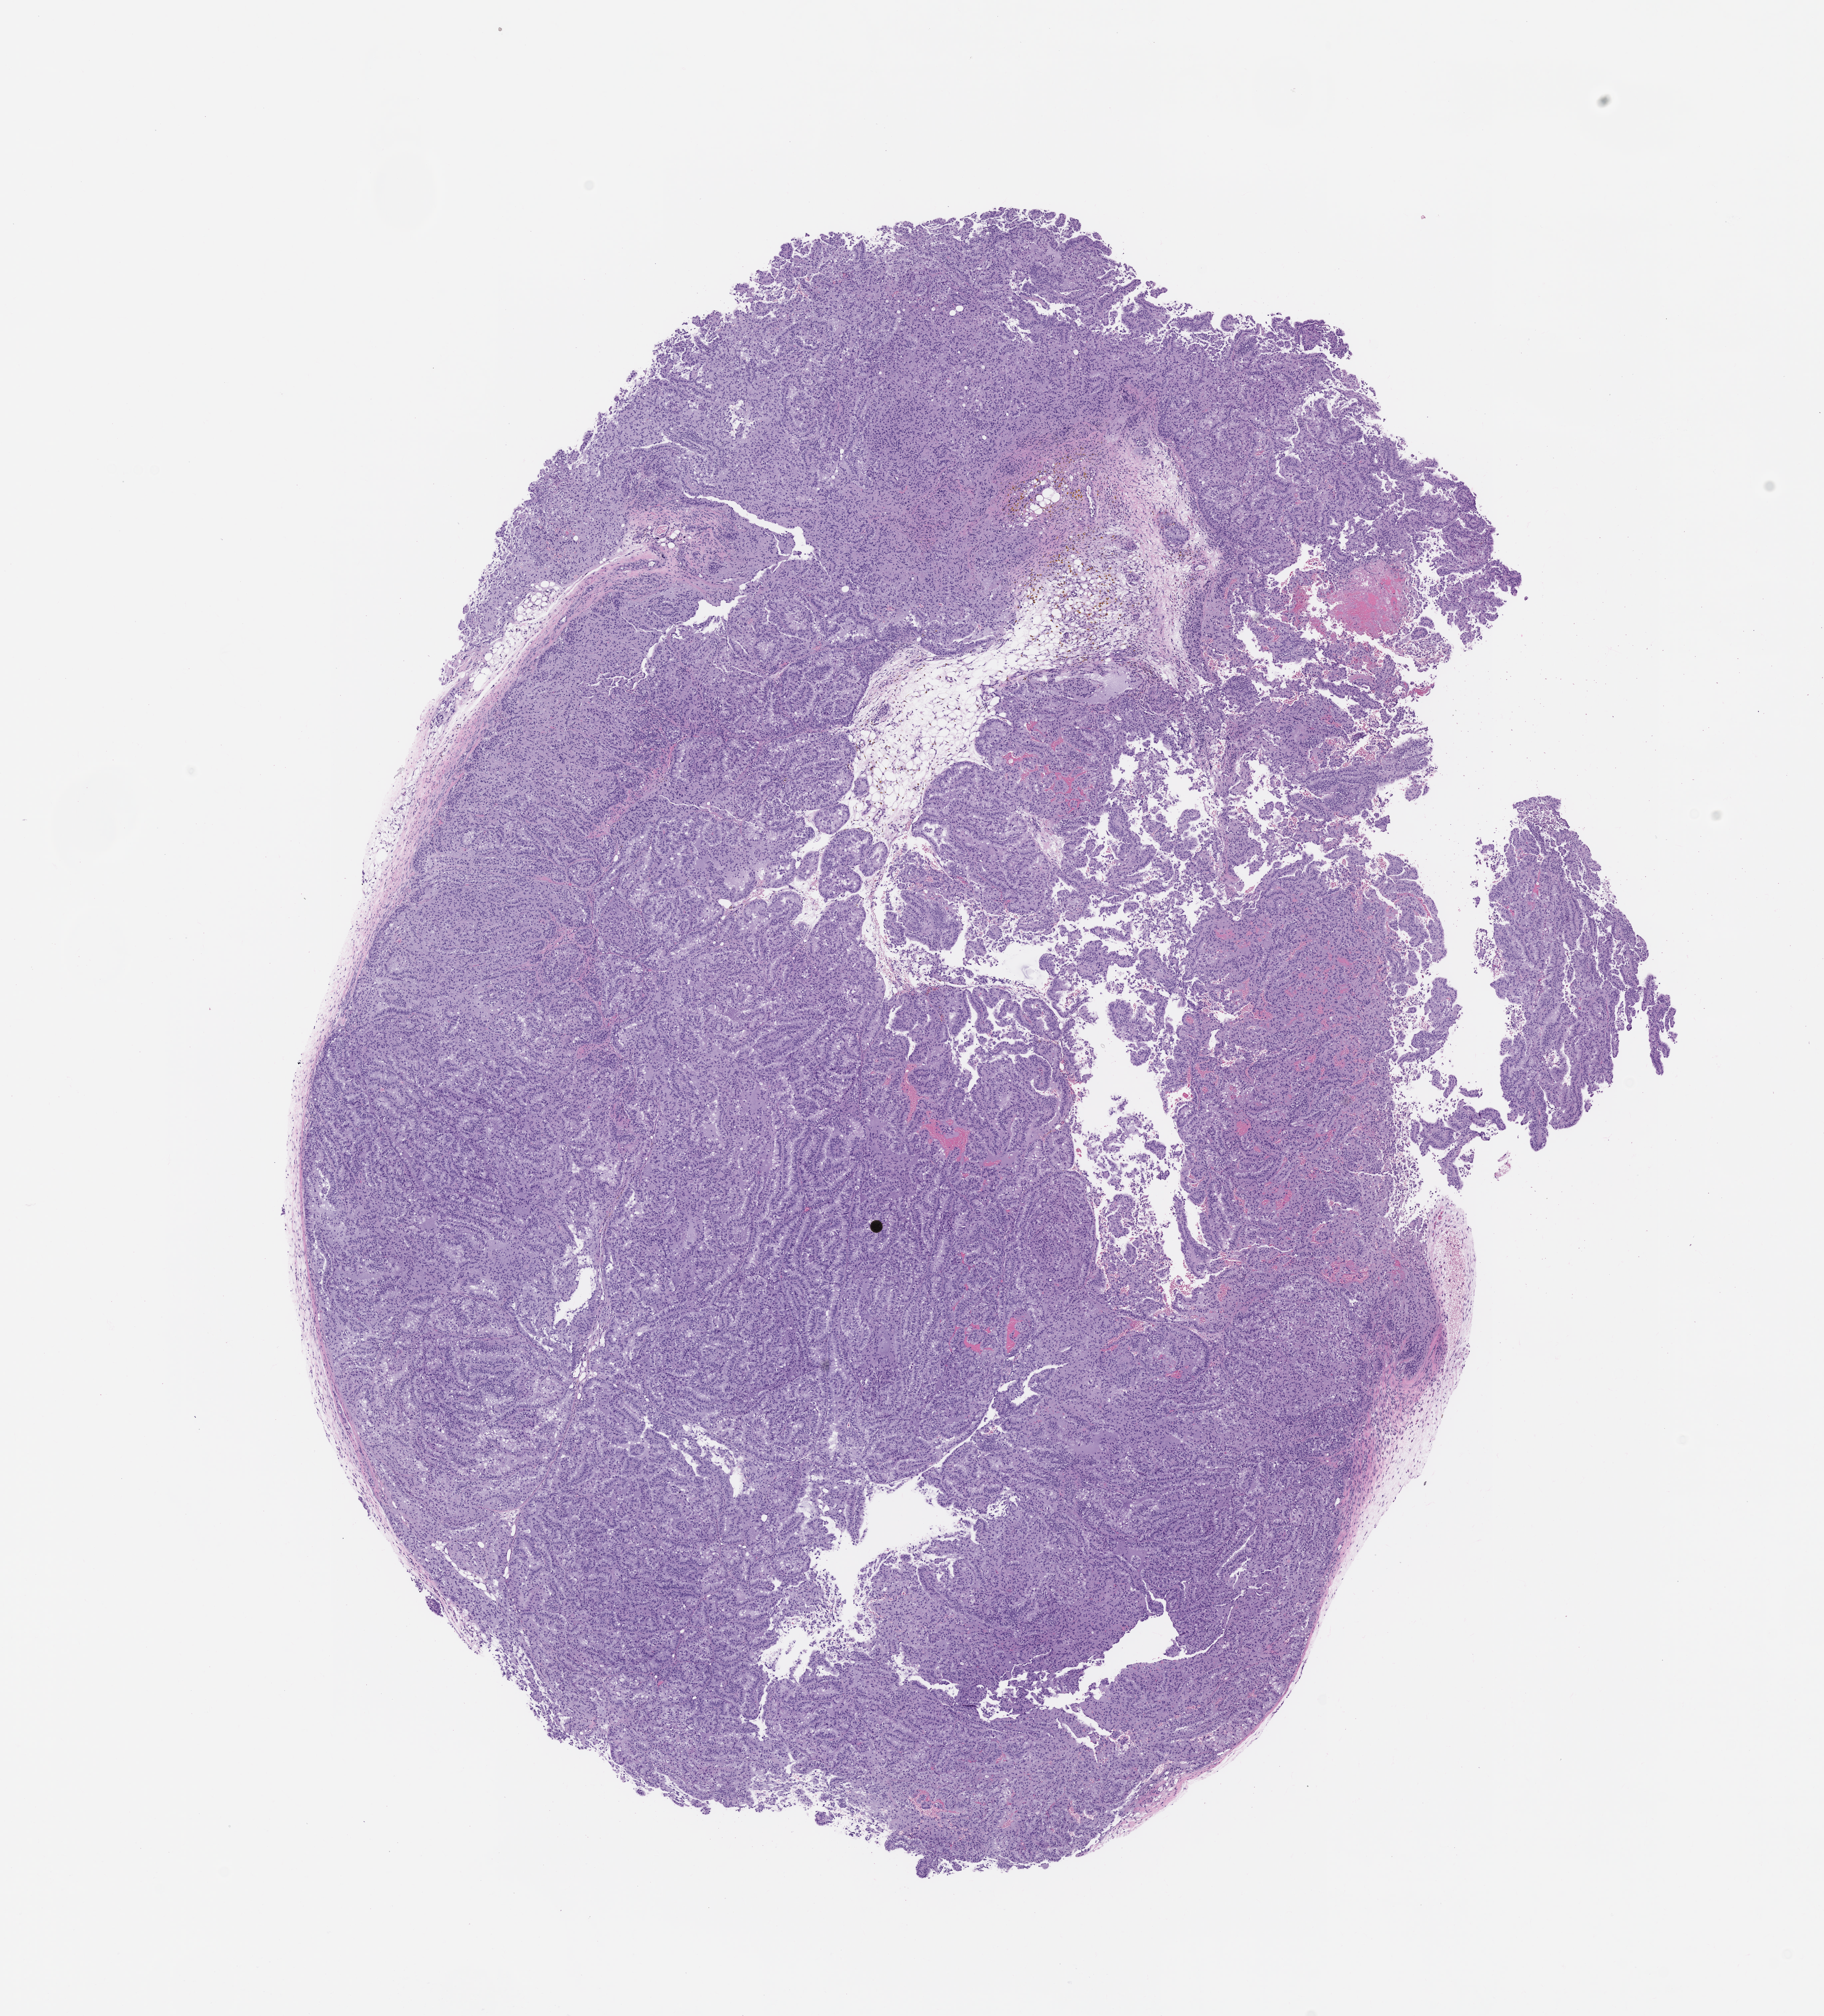
Haematoxylin and eosin whole-slide image of a patient-derived xenograft (PDX) tumor grown in a mouse, passage 0 — shown as a low-resolution overview of the whole scanned area (about 11.0 x 12.2 mm); FFPE section; tumor site category: genitourinary tract.
Originating patient diagnosis: Renal Cell Carcinoma, Not Otherwise Specified.